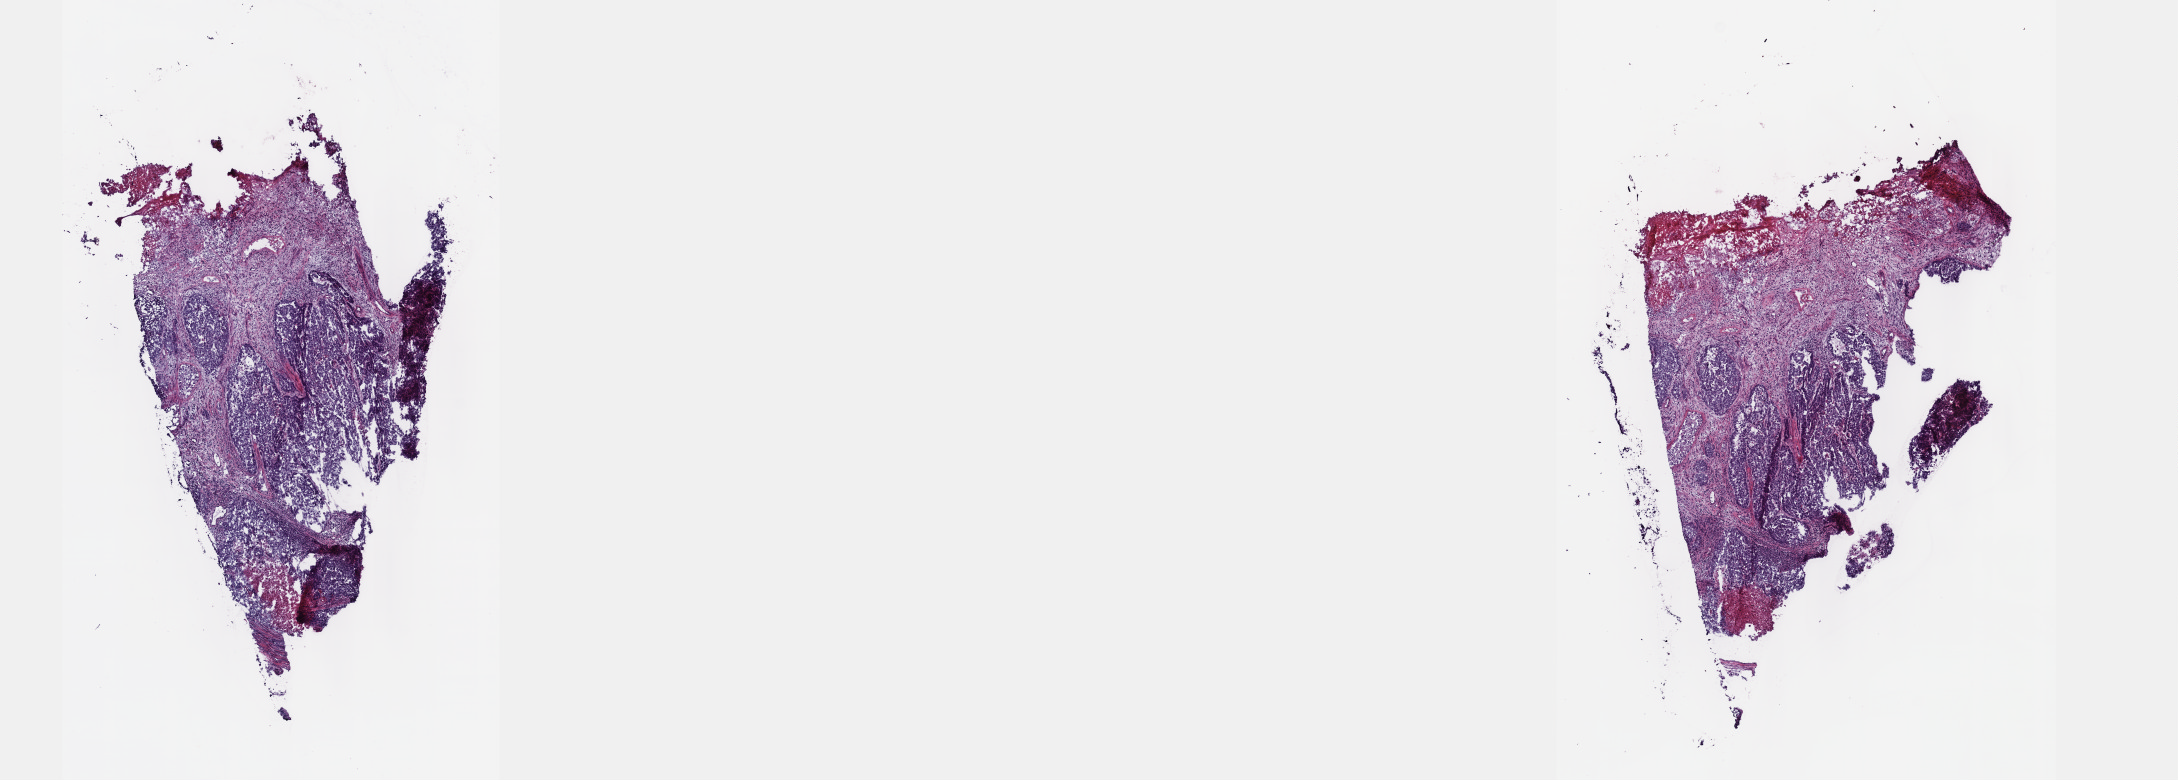
Digitized Hematoxylin and eosin (H&E) stained tissue section (whole slide), whole scanned area (about 17.6 x 6.3 mm, from a 40x scan) shown as a low-resolution overview; frozen section from the top of the tissue portion; sample: primary tumour, testis. Male, age 41 years at initial diagnosis. Pathologist review of this section (percent, as recorded): tumour cells 70%, tumour nuclei 70%, normal cells 0%, stromal cells 20%, necrosis 10%. Infiltration values recorded for this section: lymphocyte infiltration 40%, monocyte infiltration 20%, neutrophil infiltration 20%.
AJCC pathologic stage: IS (6th edition). Diagnosis: Embryonal carcinoma, NOS.